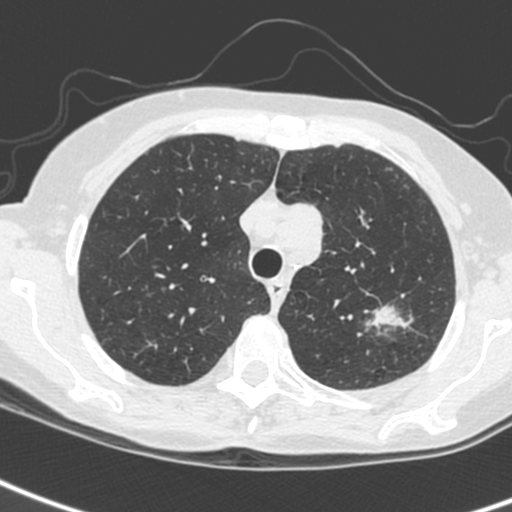
Low-dose screening chest CT, one axial slice. Slice 199 of 242 in the series (ordered by position). 120 kVp. Lung window (W 1500 / L -600 HU). 1.3 mm slice thickness. 512 × 512 image matrix.
Annotated regions visible in this slice (outlined manually by an expert reader):
- lesion 1 (tumor, upper lobe of left lung): bounding box <373,307,403,327> (left, top, right, bottom; pixels)
- lesion 3 (tumor, upper lobe of left lung): <294,203,323,263>